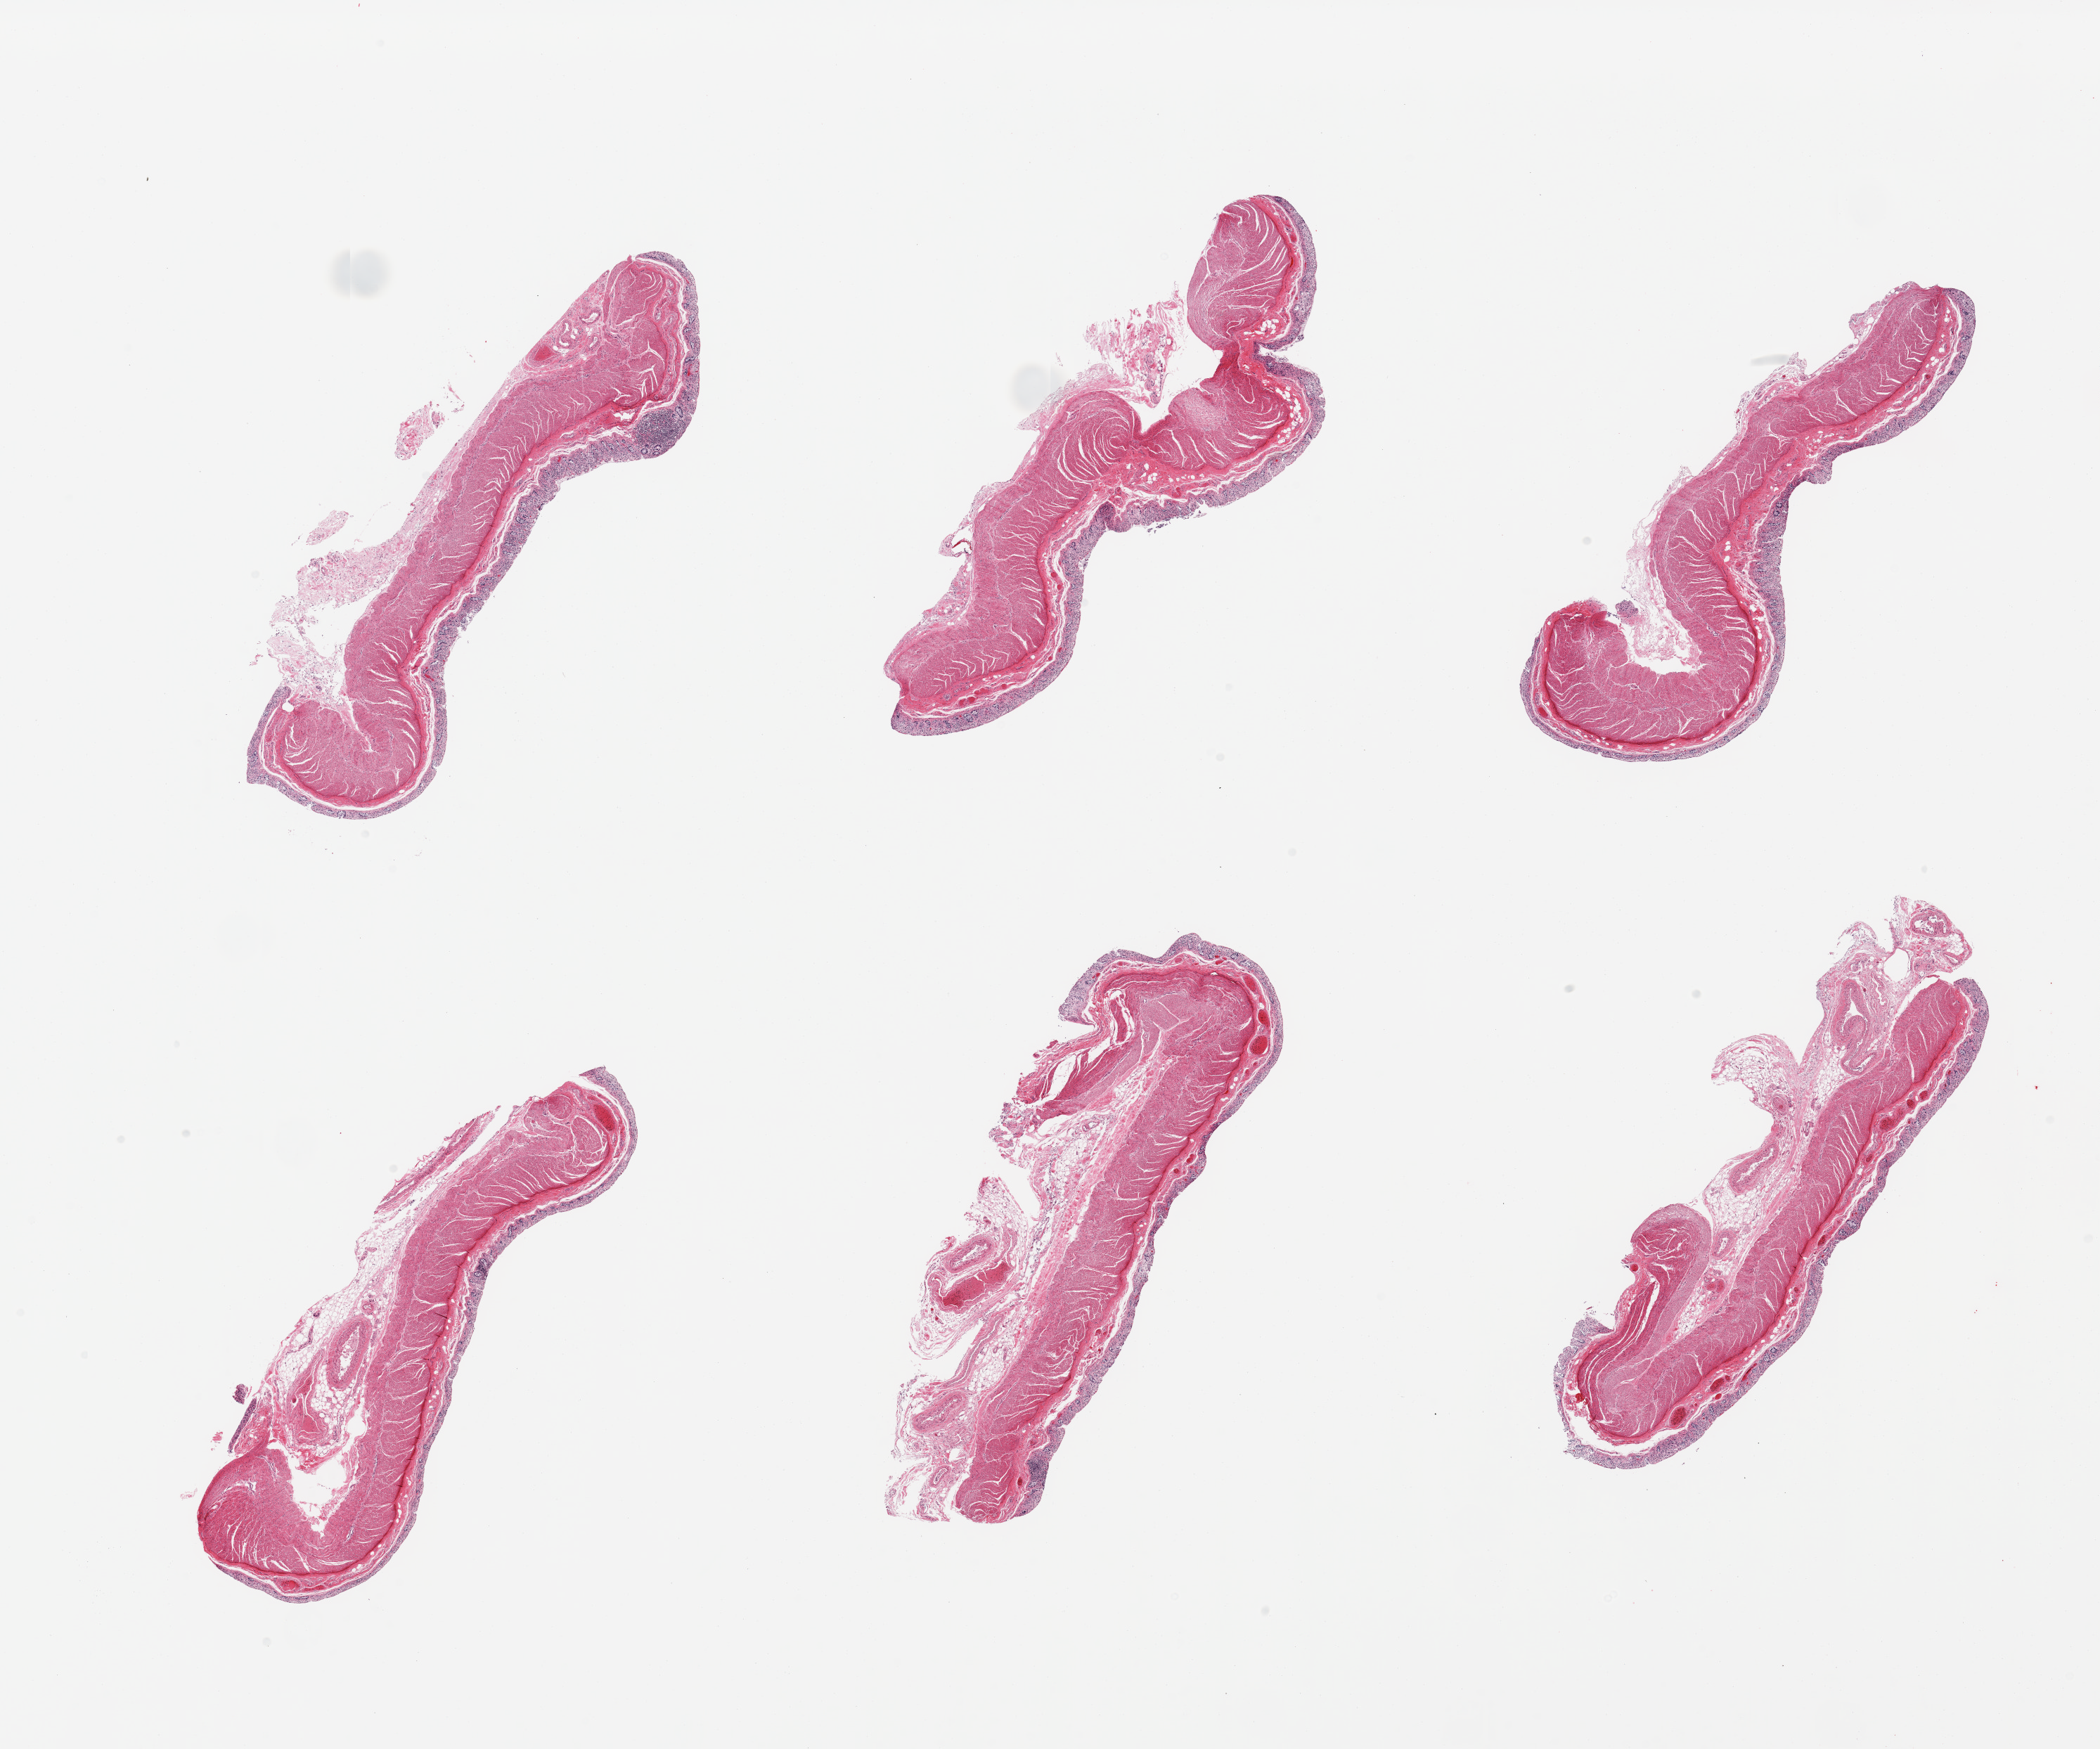
Digitized hematoxylin and eosin (H&E)-stained section, brightfield, whole scanned area (about 23.6 x 19.7 mm, from a 20x scan) shown as a low-resolution overview. PAXgene-fixed paraffin-embedded (PFPE) section. Section of transverse colon (target tissue). Tissue donor sample. Donor: female.
Pathologist's review note for this sample: 6 pieces, mucosa totally autolyzed.